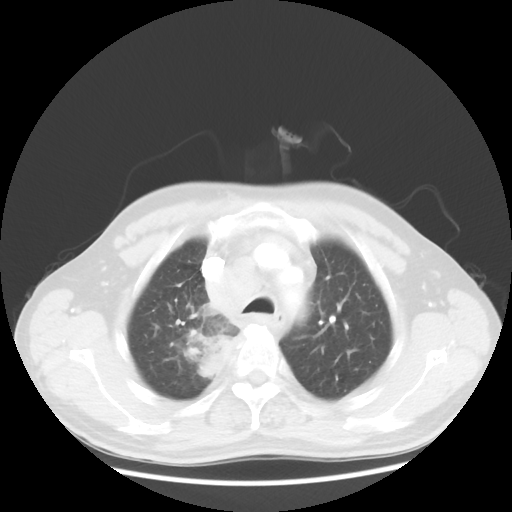
Chest CT, one axial slice. Slice 97 of 124 in the series (ordered by position). 100 kVp. Lung window (W 1500 / L -600 HU). 5 mm slice thickness. 512 × 512 image matrix, field of view 382 × 382 mm. Patient: male, 64 years. Case-level facts recorded for this patient, not image findings: clinical TNM (as recorded): T3 N3 M0; histopathological grade: G3.
Outlined on this slice (bounding box drawn by a radiologist):
- lung tumour (recorded histology: small cell carcinoma): bounding box (x1, y1, x2, y2) in pixels: (184, 303, 239, 386)